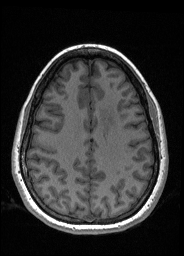
Pre-operative brain MRI before brain-tumour surgery, one axial slice. Slice 68 of 176 in the series (ordered by position). T1-weighted post-contrast. 184 × 256 image matrix. From the clinical record (not read from this slice): histopathology: Oligodendroglioma; WHO grade: 2; IDH mutation: yes; tumour location: Left Frontal.
Outlined on this slice (manually delineated by an expert):
- tumour: bounding box [x1, y1, x2, y2] px = [100, 107, 116, 126]